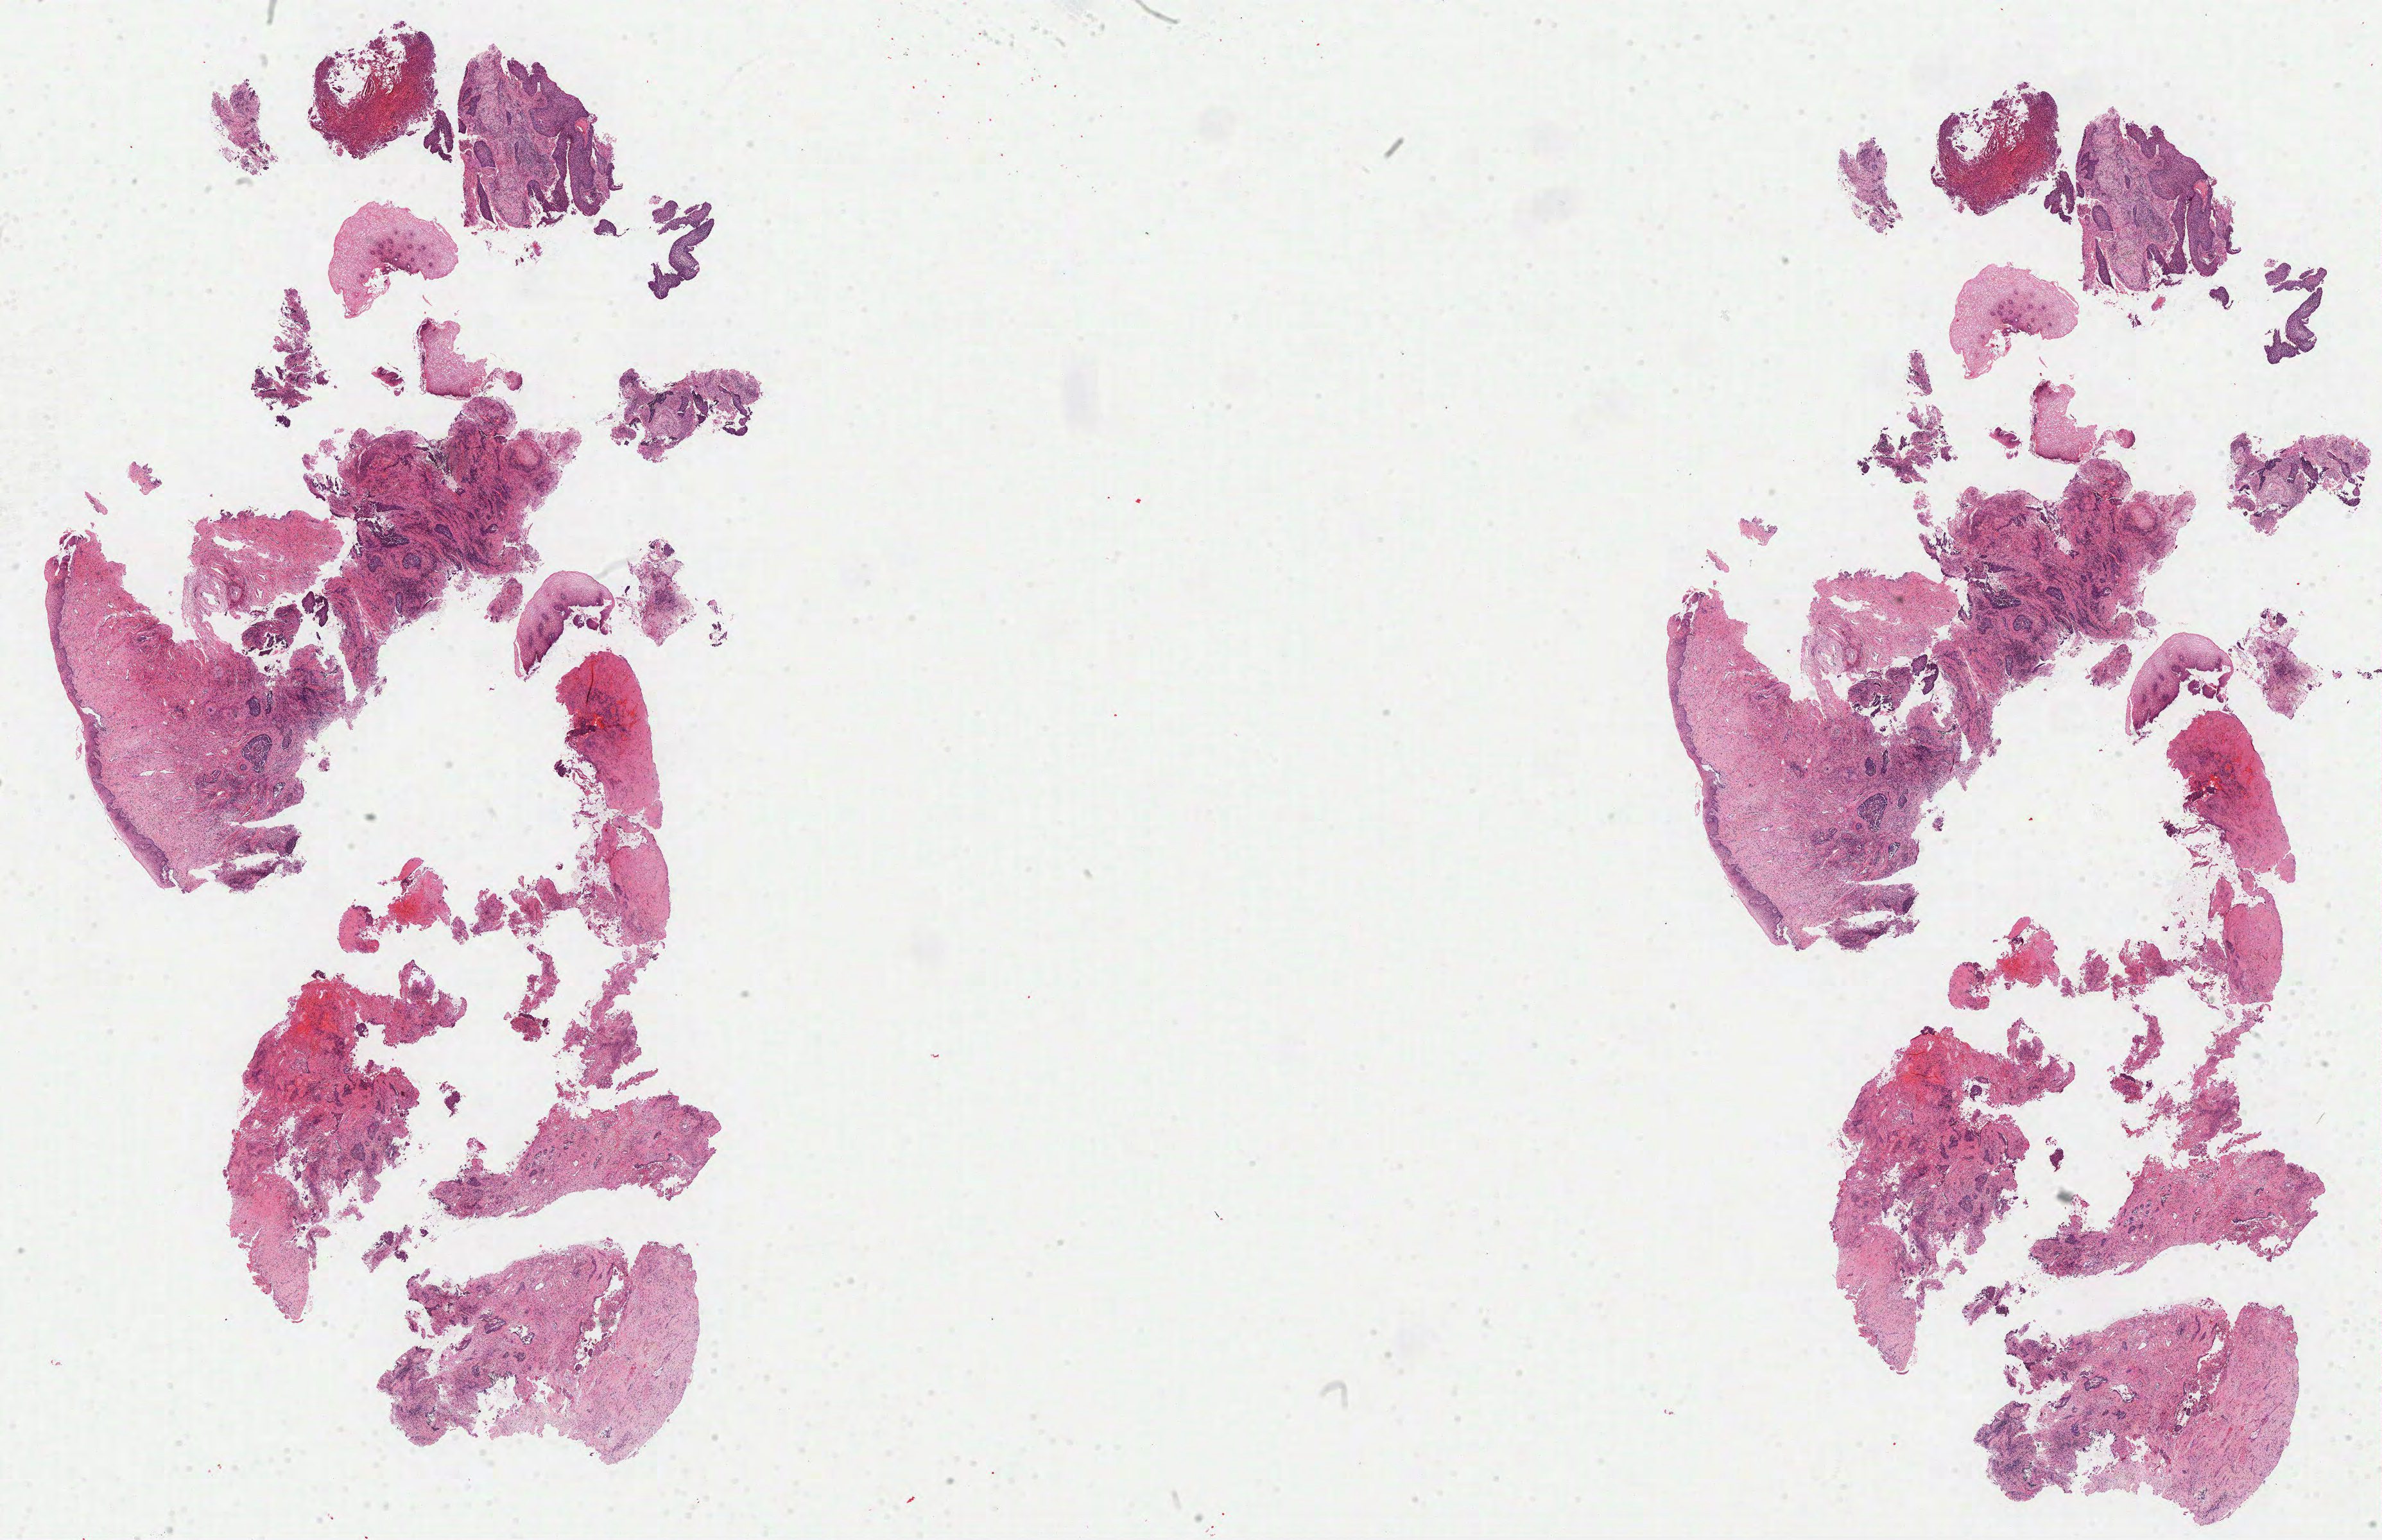
H&E-stained whole-slide image — low-resolution overview of the scanned area, about 29.9 x 19.3 mm. Formalin-fixed paraffin-embedded (FFPE) diagnostic section. Sample: primary tumour, cervix. Female, age 35 years at initial diagnosis. Histologic grade: G2 (moderately differentiated).
• diagnosis: Squamous cell carcinoma, large cell, nonkeratinizing, NOS
• FIGO stage: IIIB